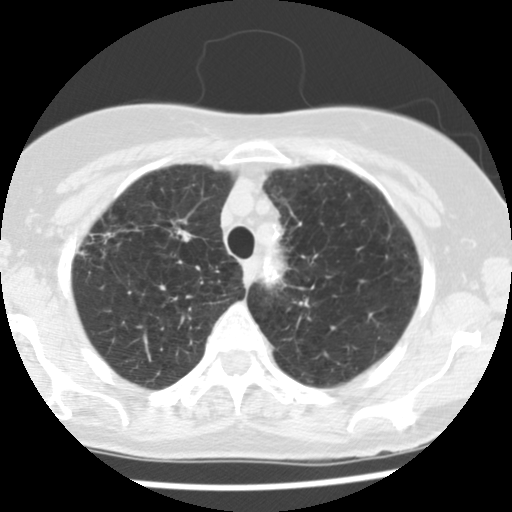
Chest CT (low-dose screening protocol), one axial image; first (baseline) screen; lung window (W 1500 / L -600 HU); standard (soft-tissue) reconstruction kernel (STANDARD); slice 25 of 121 in the series. Female participant, aged 70 years at enrolment.
Expert reader's lesion annotation, box from (x=151, y=204) to (x=212, y=257) px. Reader record for this screening exam (exam-level; its link to the box is not recorded): non-calcified nodule or mass ≥4 mm, left upper lobe, 8 × 6 mm, poorly defined margins, soft tissue attenuation. Note: the box lies in the patient's right hemithorax on this image, whereas the reader's record names the left lung; they may be different findings. Later outcome: lung cancer diagnosed 745 days after this screen — non-small cell carcinoma, right upper lobe, stage IV (AJCC 6th edition), 30 mm at pathology.